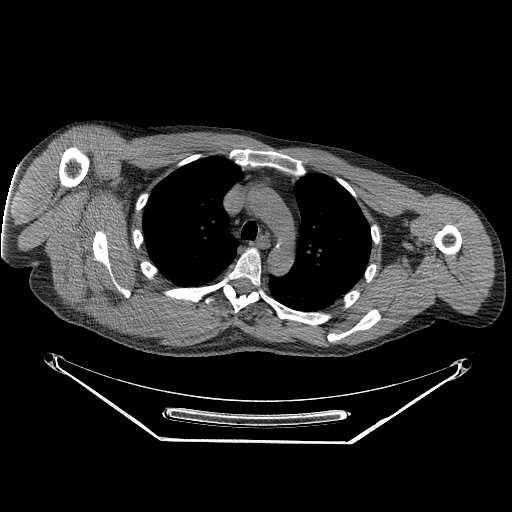
CT of an extremity soft-tissue mass (from a PET/CT study), one axial slice; position 186 of 267 along the scan axis; reconstruction kernel STANDARD; 140 kVp; soft-tissue window (W 400 / L 40 HU); 3.75 mm slice thickness; 512 × 512 image matrix. Male patient. From the clinical record (not read from this slice): histological type: pleiomorphic spindle cell undifferentiated; grade: high; site of the primary tumour: right parascapusular.
Annotated regions visible in this slice (expert contour drawn on MRI and transferred to this co-registered scan by the dataset authors):
- gross tumour volume including surrounding oedema: bounding box <82,274,220,337> (left, top, right, bottom; pixels)
- gross tumour volume (mass): <87,276,200,334>